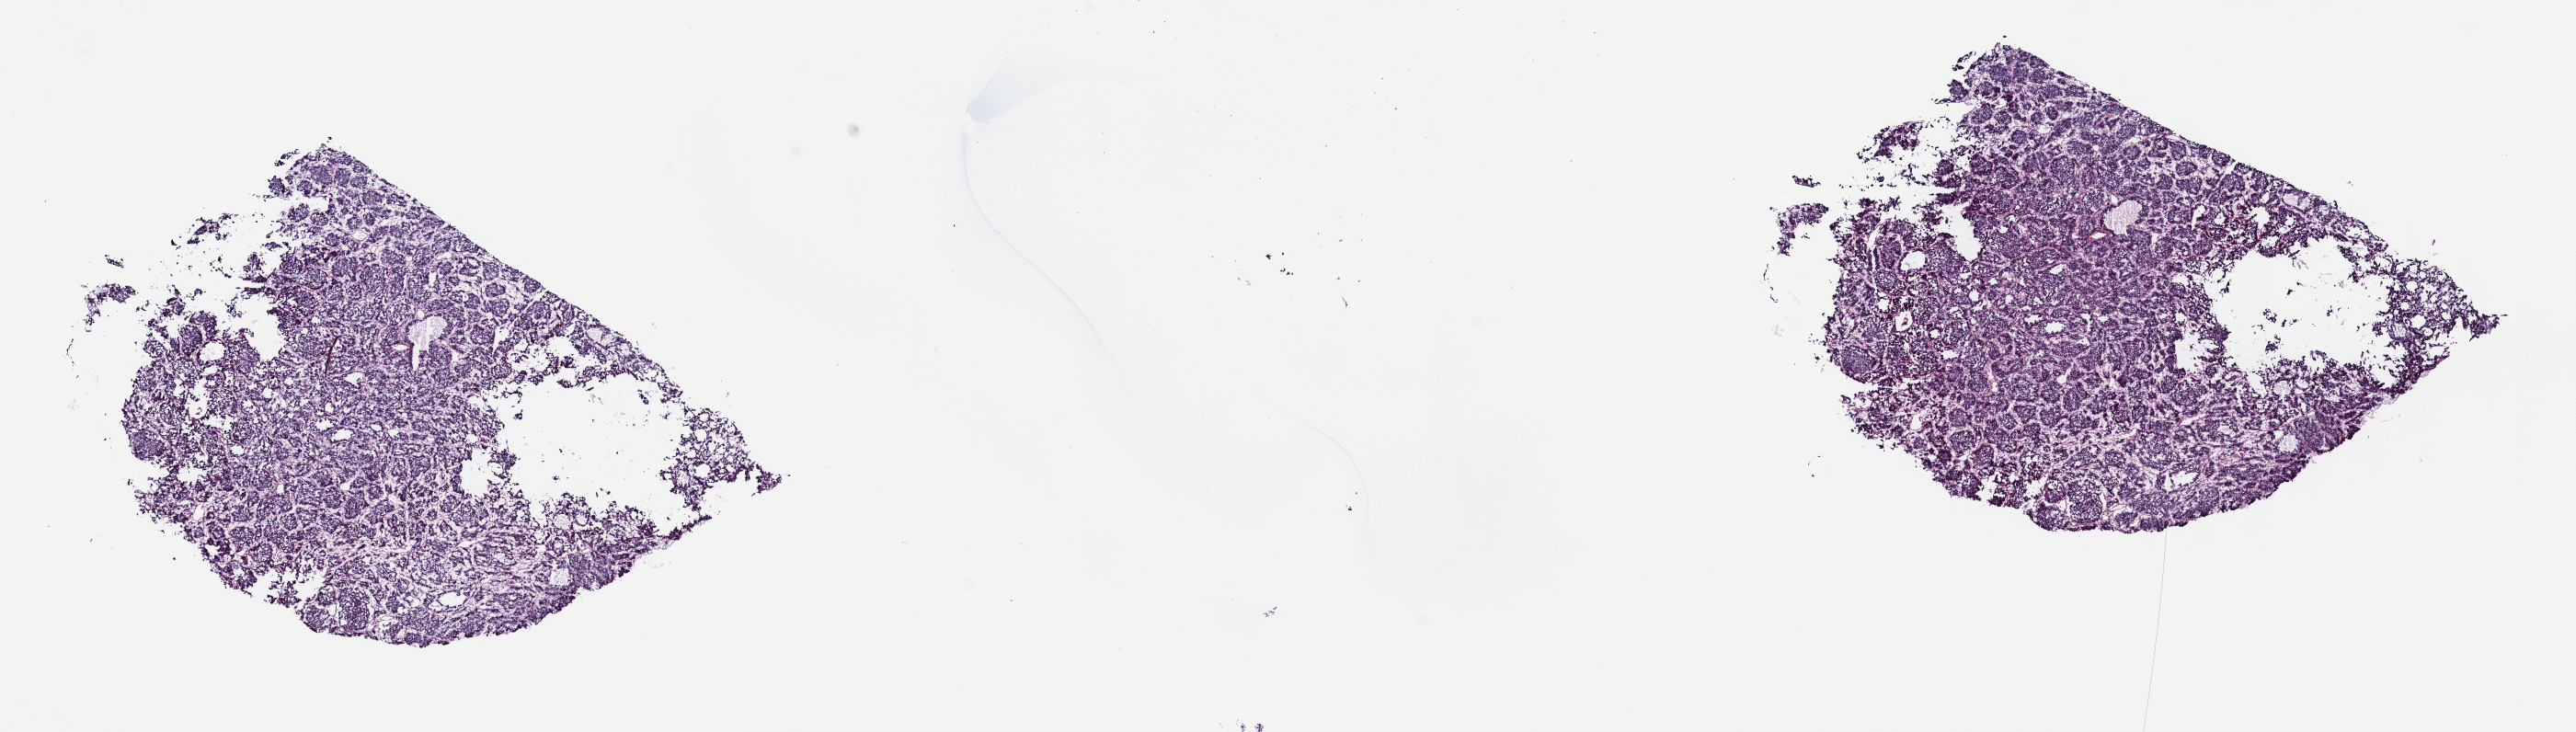
H&E whole-slide image, whole scanned area (about 22.7 x 6.4 mm) shown as a low-resolution overview. Frozen section from the top of the tissue portion. Primary tumour sample from the pancreas. Female patient; age at initial diagnosis 64 years. Histologic grade: G1 (well differentiated). Slide review estimates, as recorded: tumour cells 100%, tumour nuclei 90%, normal cells 0%, stromal cells 0%, necrosis 0%. Inflammatory infiltration, as recorded: lymphocyte infiltration 0%, monocyte infiltration 0%, neutrophil infiltration 0%.
- TNM: T2 N0 MX
- AJCC pathologic stage: IB
- pathologic diagnosis: Neuroendocrine carcinoma, NOS (tail of pancreas)